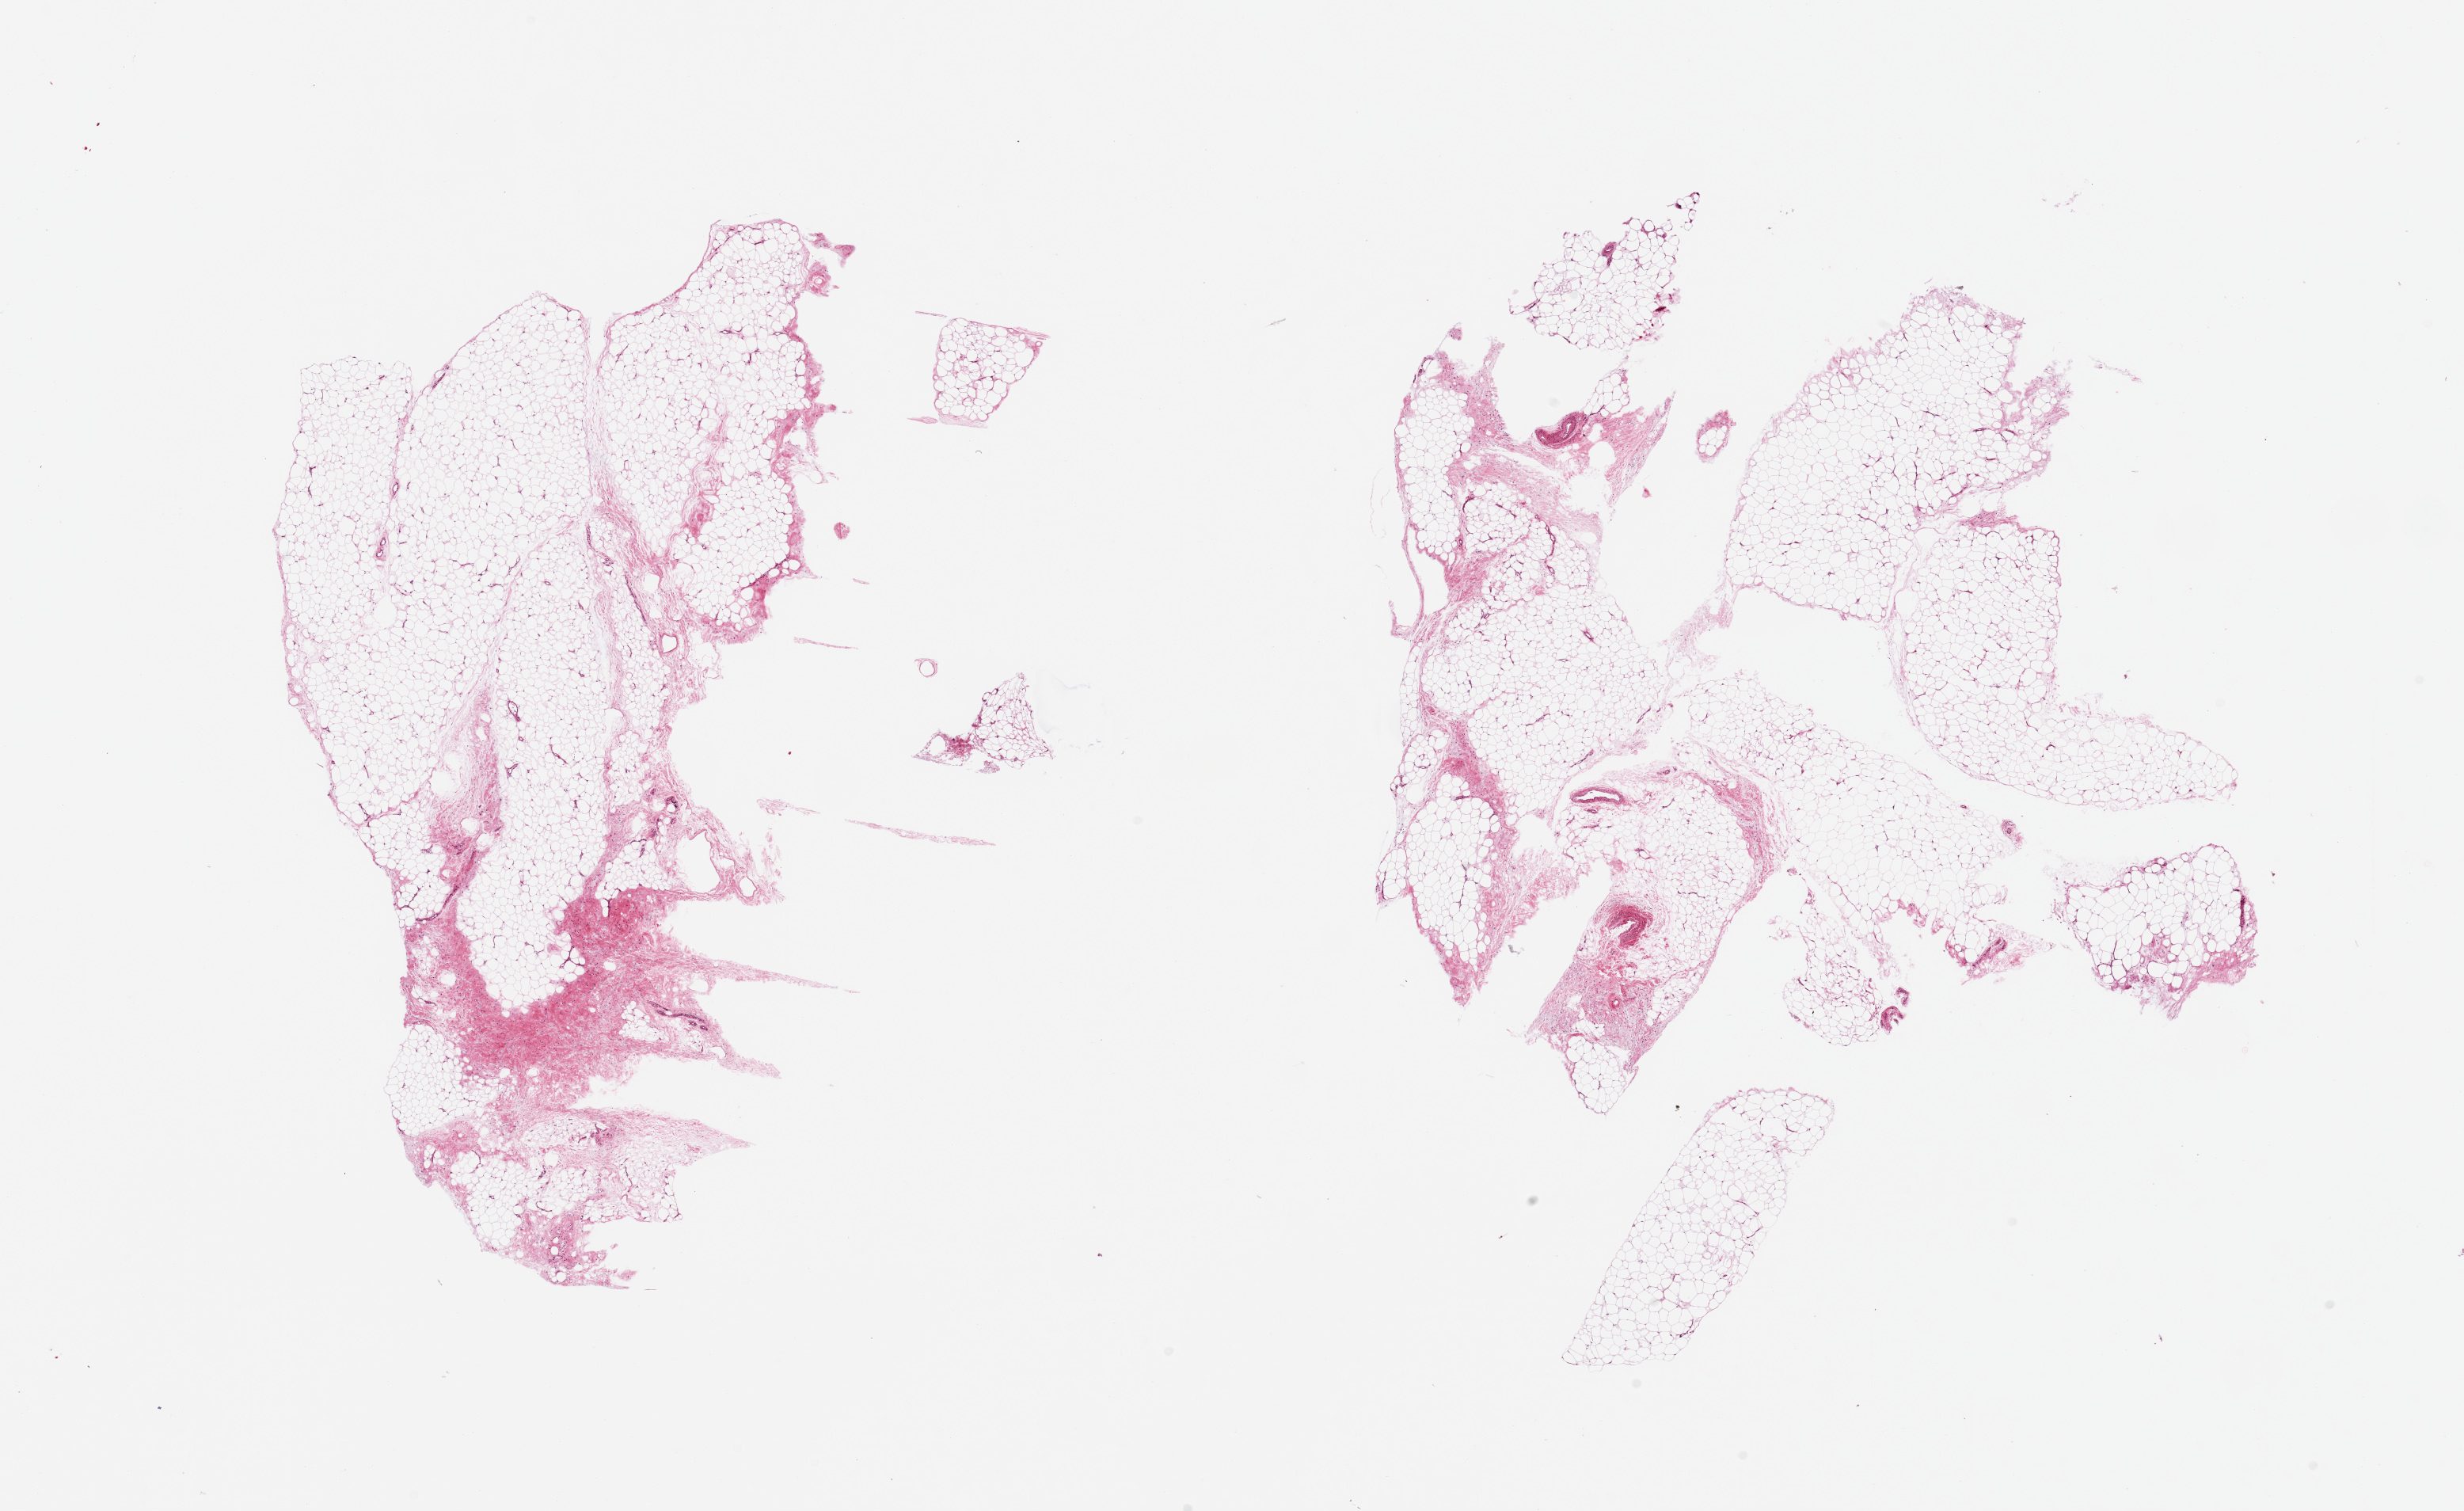
Hematoxylin and eosin (H&E) whole-slide image, low-resolution overview of the scanned area, about 24.6 x 15.1 mm (slide scanned at 20x); PAXgene-fixed, paraffin-embedded tissue; sampled site (target tissue): adipose tissue; donor tissue sample. Donor sex: female.
Reviewer comment on this tissue sample: 2 pieces; mature adipose tissue and fibrovascular component.